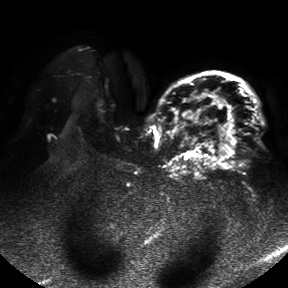
Breast MRI, one axial slice; position 32 of 50 along the scan axis; diffusion-weighted series; image 2 of 4 stored at this slice position (different b-values; order by instance number); 1.5 T; 4 mm slice thickness; 288 × 288 image matrix, field of view 390 × 390 mm. Female patient.
Outlined on this slice (manually delineated by an expert):
- tumour on diffusion-weighted imaging: bounding box <189,94,235,160> (left, top, right, bottom; pixels)